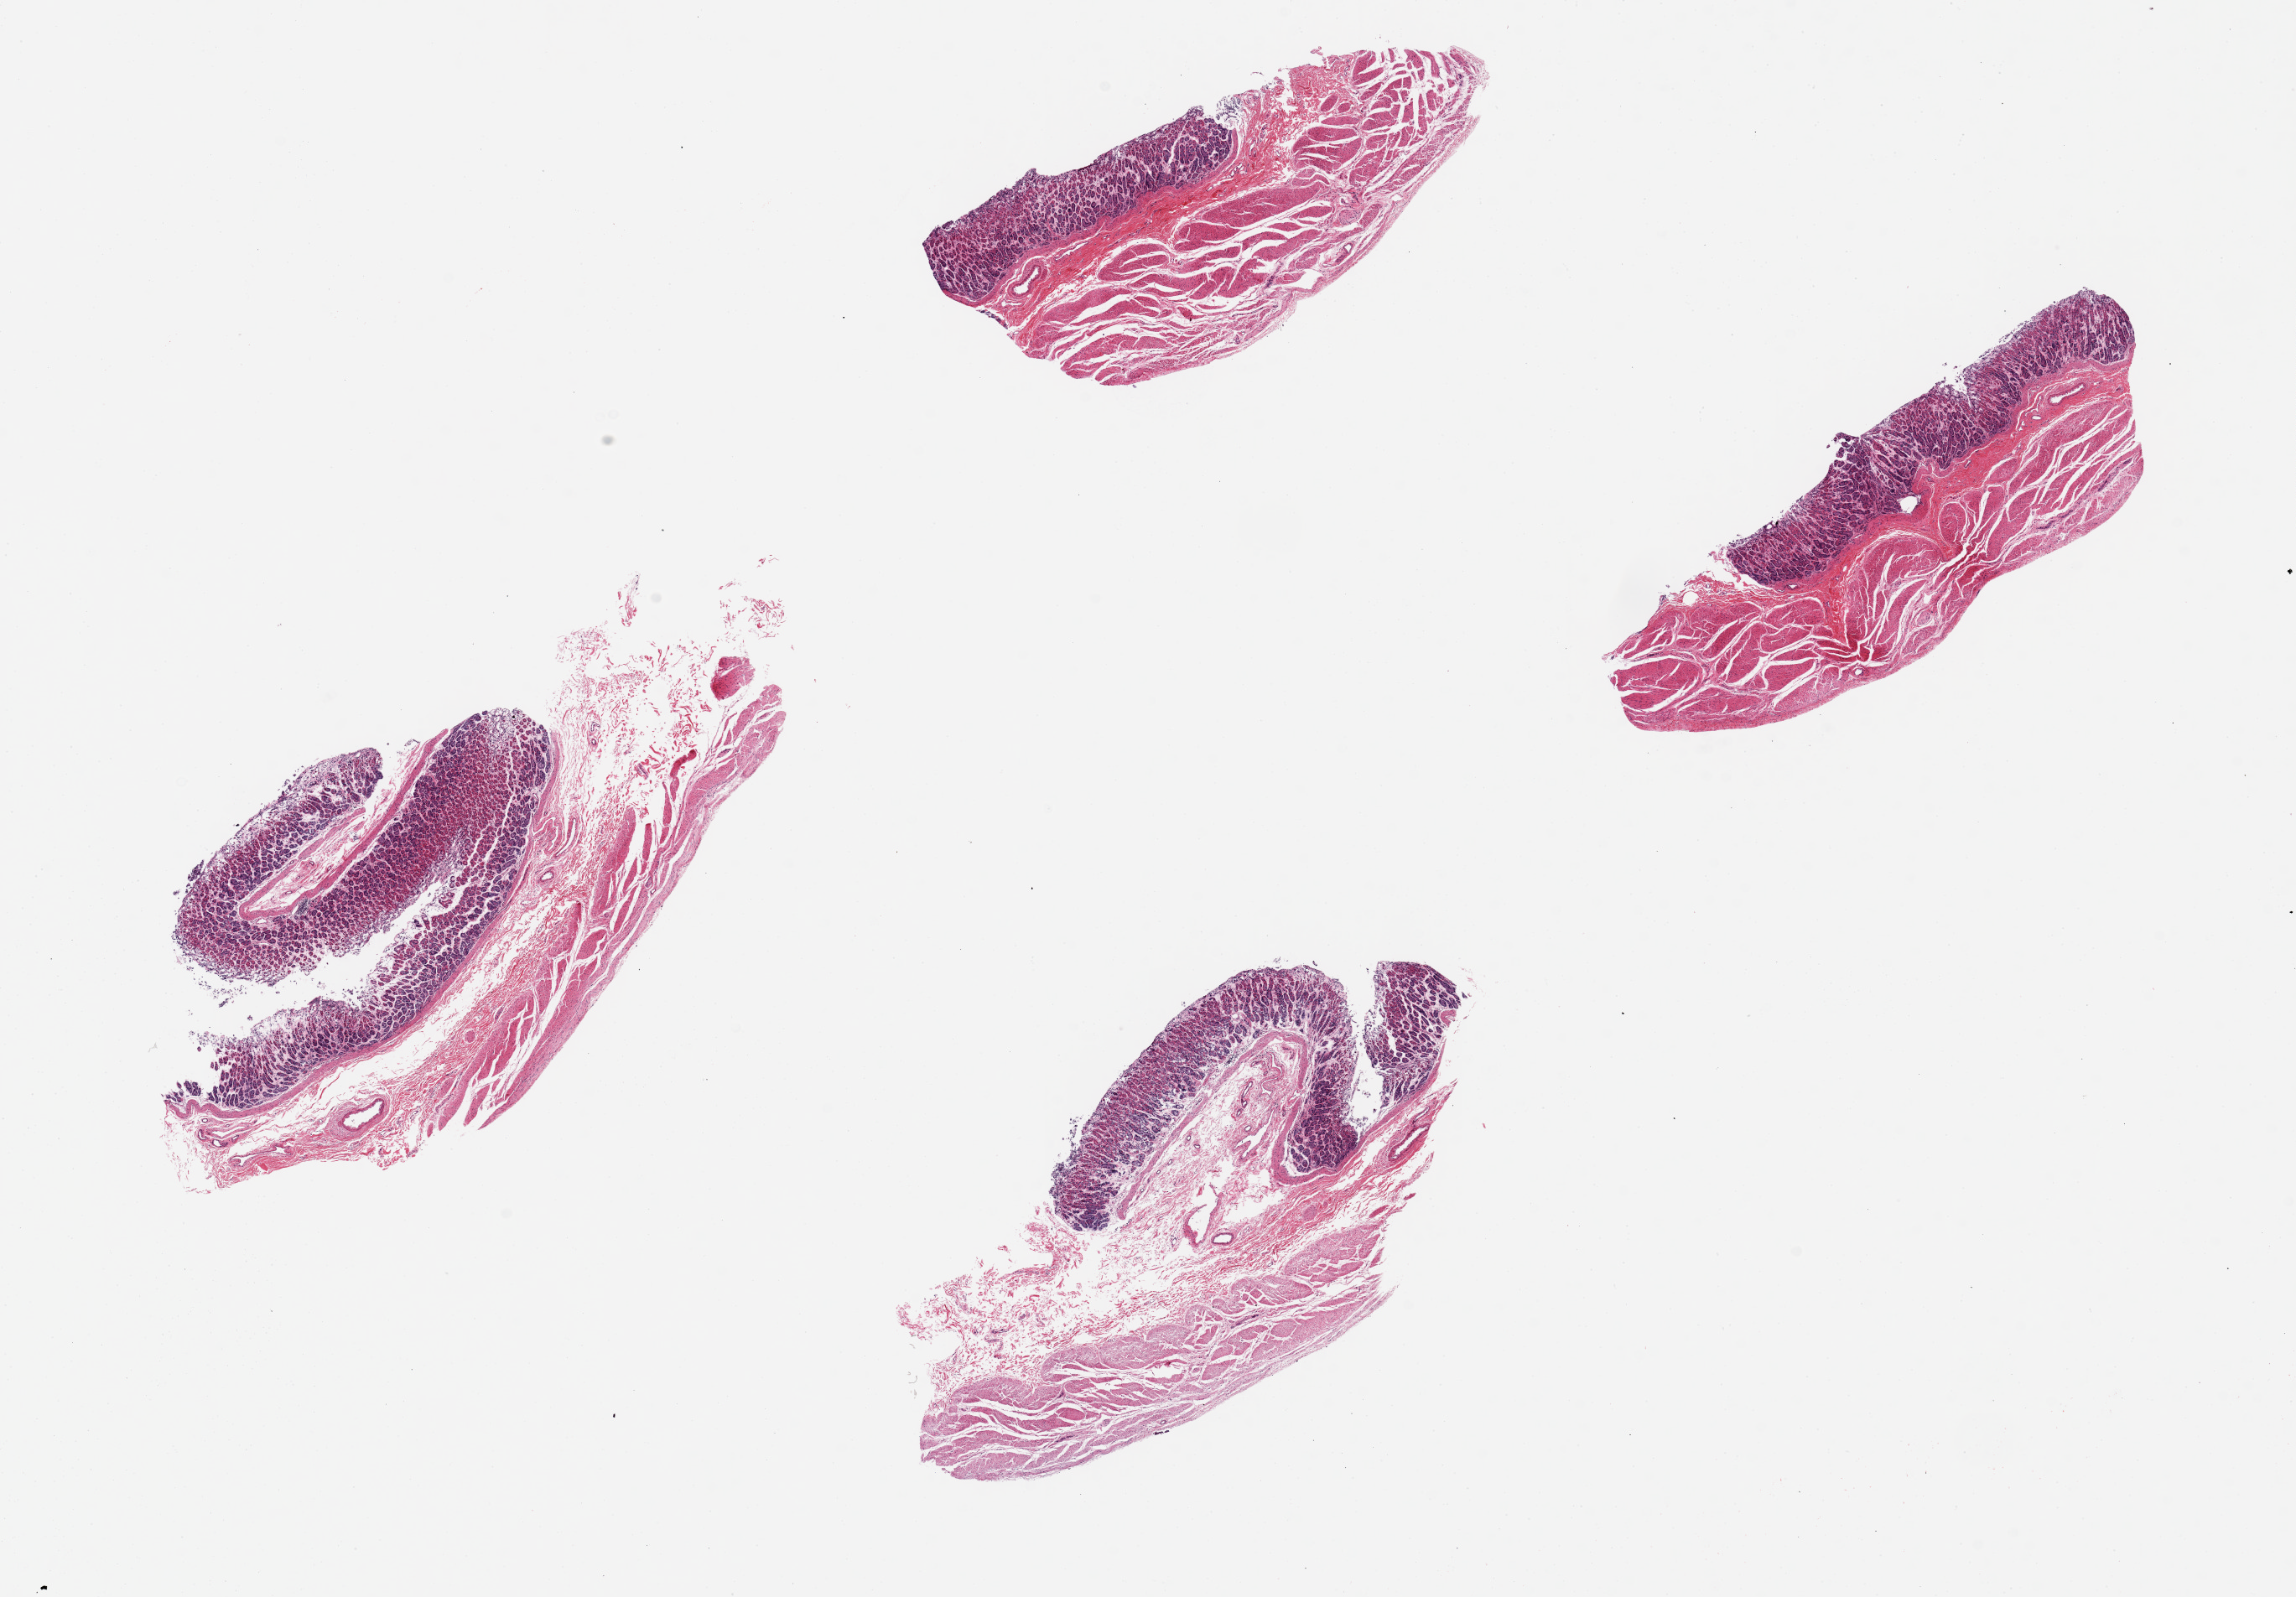
H&E whole-slide image, shown as a low-resolution overview of the whole scanned area (about 21.7 x 15.1 mm, from a 20x scan); PAXgene-fixed paraffin-embedded (PFPE) section; target tissue: stomach; tissue donor sample. Male donor.
Review note (as recorded): 4 pieces, up to 8x4mm; good oxyntic glands, but superficial glands sloughed.